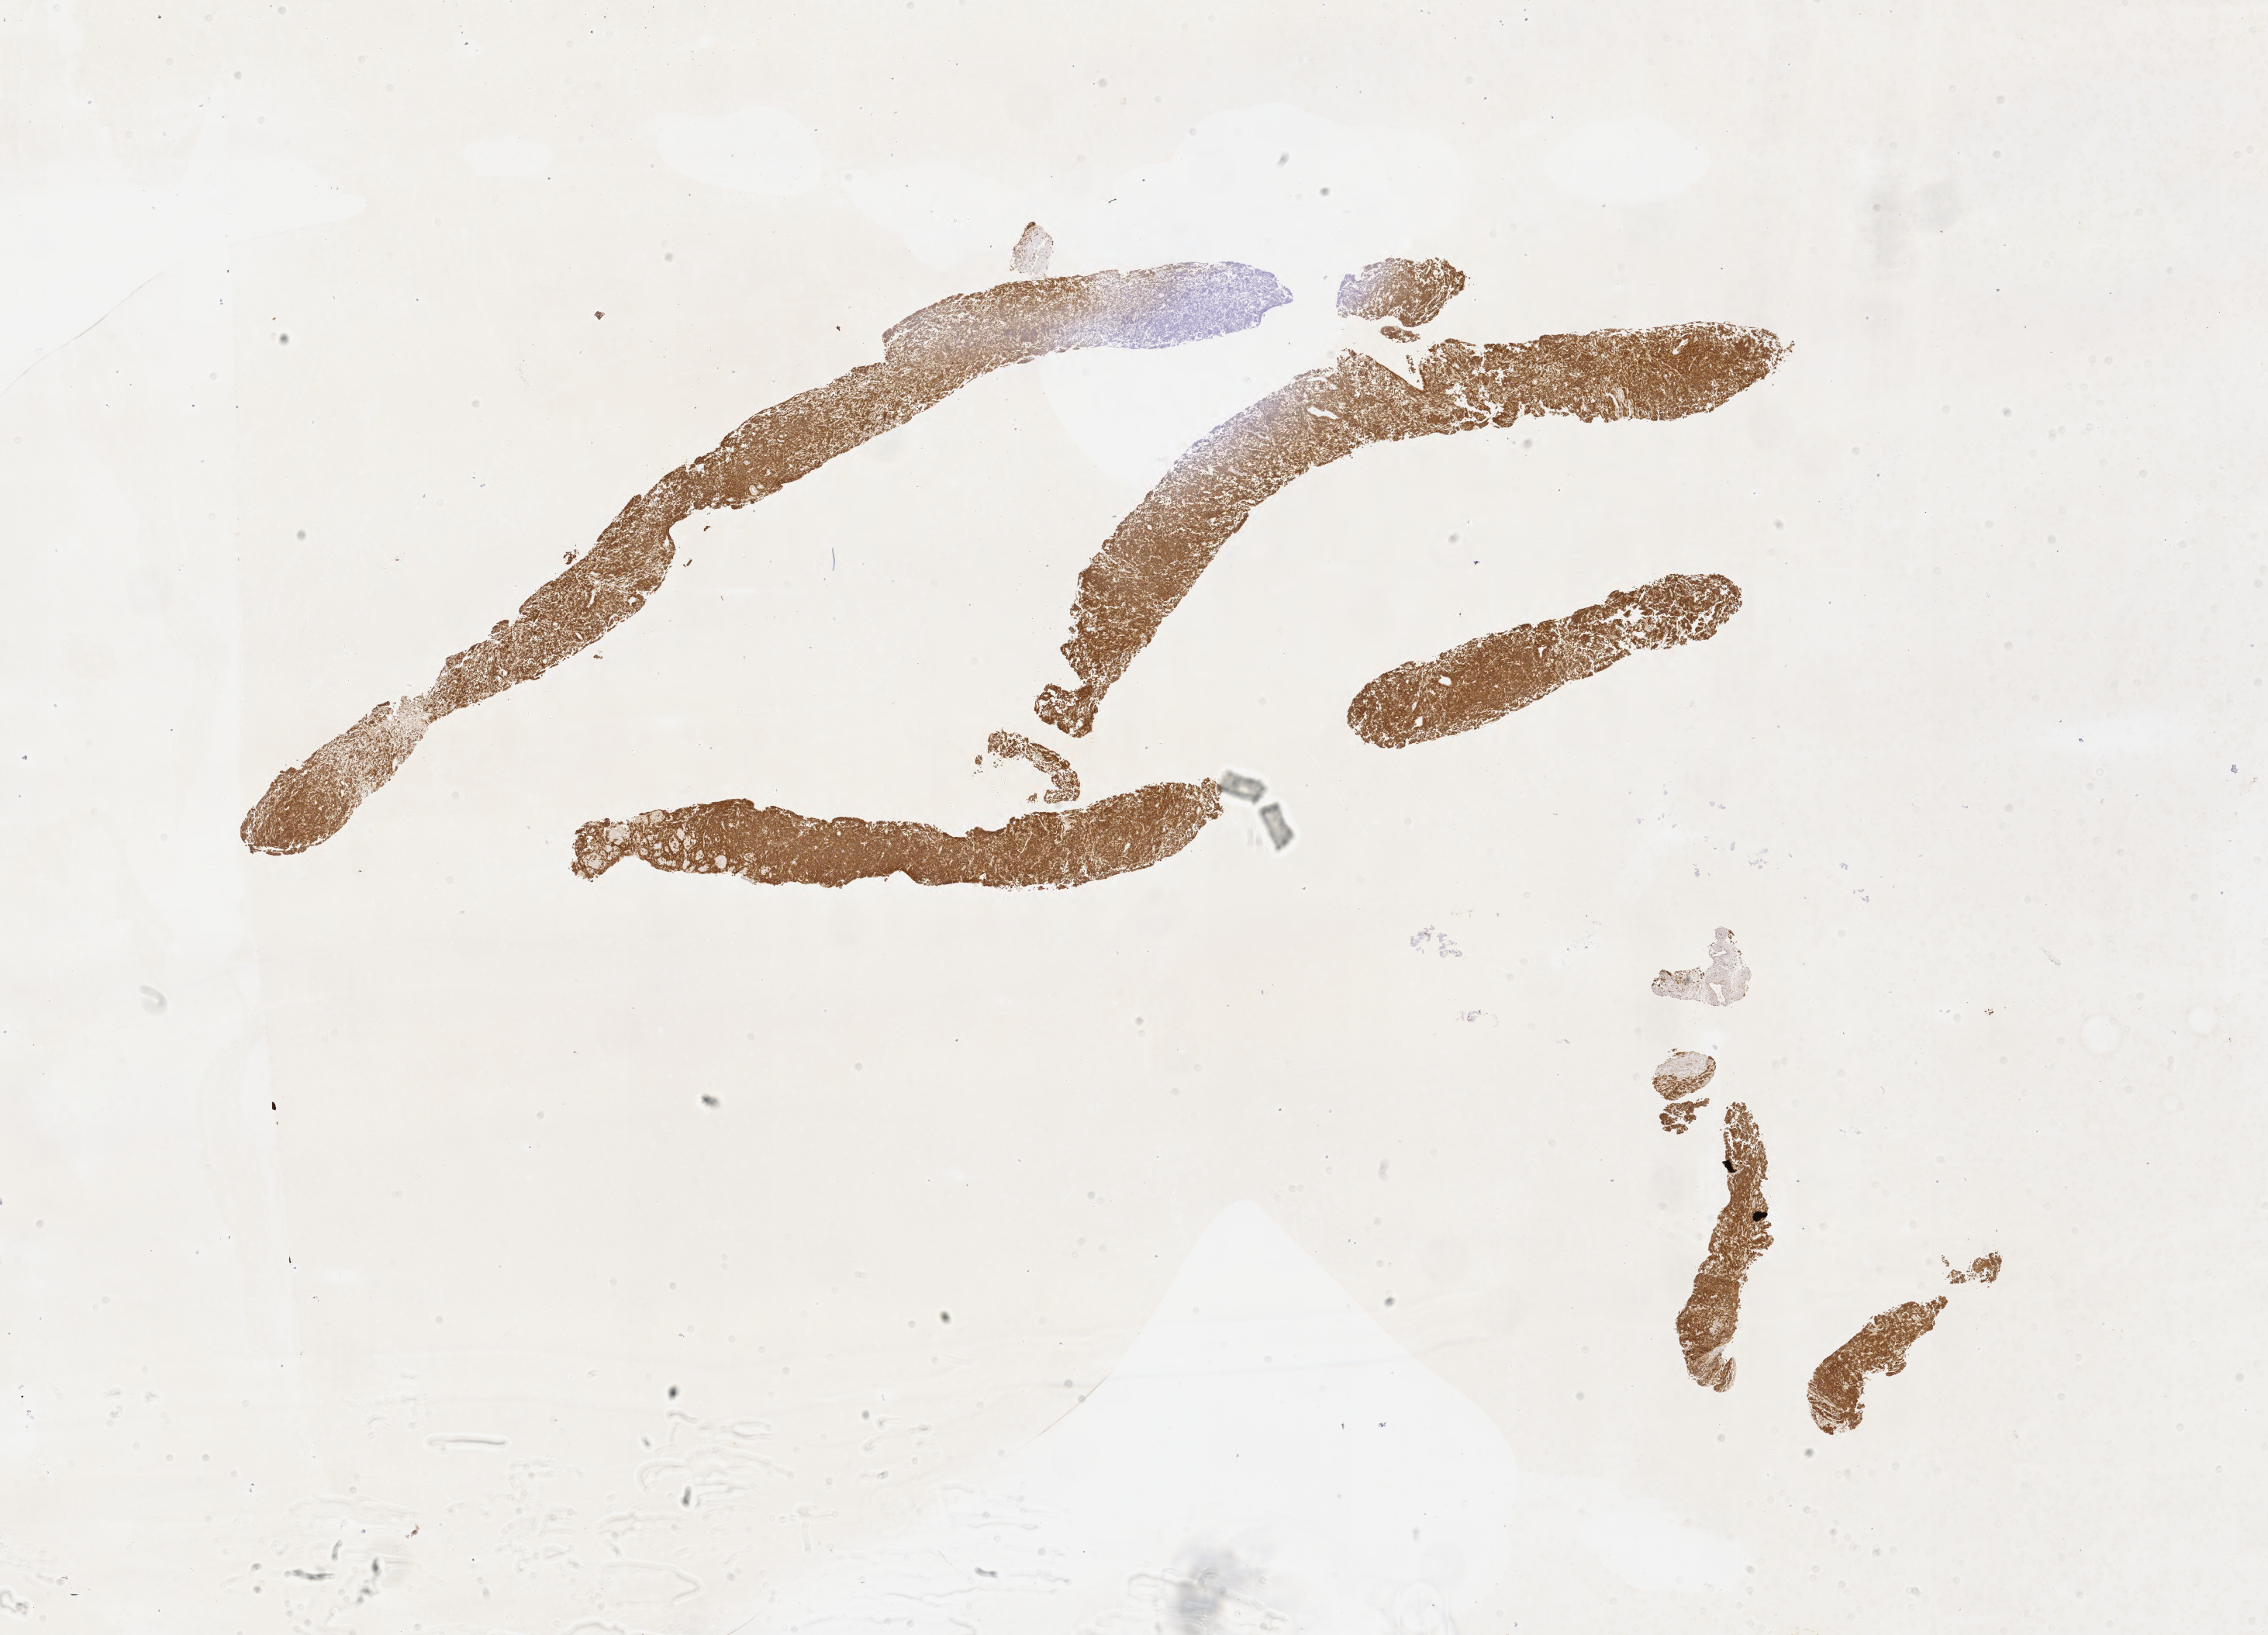
IHC for CD79a, whole-slide image — whole scanned area (about 23.6 x 17.0 mm) shown as a low-resolution overview, tumor tissue. Patient: male, aged 66.
Diagnosis: Burkitt lymphoma, NOS.